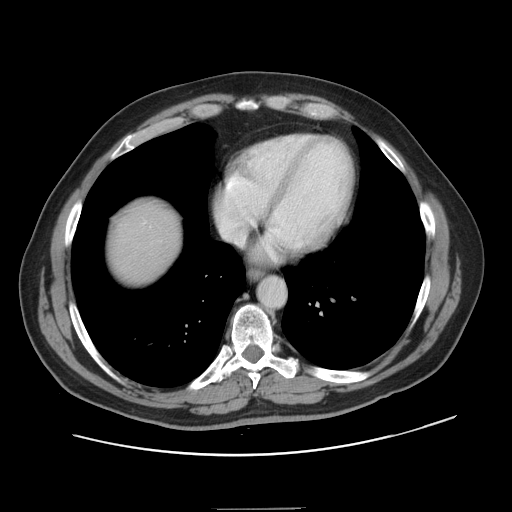
Contrast-enhanced abdominal CT, one axial slice; position 139 of 143 along the scan axis; intravenous contrast given; soft-tissue window (W 400 / L 40 HU); 2.5 mm slice thickness; 512 × 512 image matrix, field of view 402 × 402 mm. Male patient, age 62 years. Case-level facts recorded for this patient, not image findings: diagnosis: colorectal cancer liver metastases, imaged before liver resection; multiple liver metastases: yes; largest metastasis: 2.7 cm; disease in both lobes: no.
Structures marked on this image (expert manual segmentation):
- liver: bounding box [x1, y1, x2, y2] px = [110, 206, 180, 283]
- planned liver remnant (the part of the liver to remain after resection): [109, 207, 180, 283]